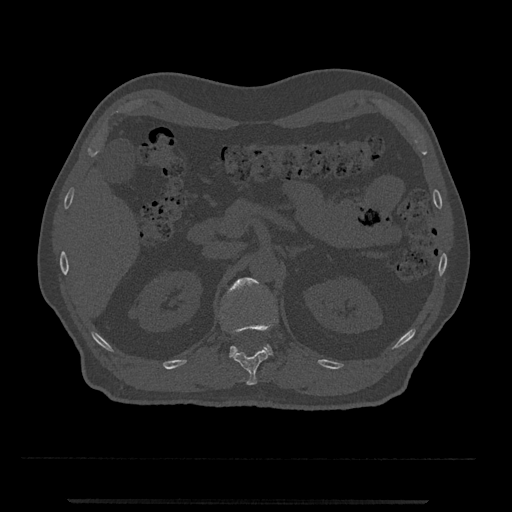
CT including the spine, one axial slice. Slice 374 of 797 in the series (ordered by position). Reconstruction kernel Br40s/3. Bone window (W 1800 / L 400 HU). 0.5 mm slice thickness. 512 × 512 image matrix. Male patient, age 63 years. Case-level facts recorded for this patient, not image findings: primary cancer: prostate.
Outlined on this slice (semi-automatic segmentation, software-assisted and operator-edited):
- L1 vertebra: bounding box [x1, y1, x2, y2] px = [227, 277, 275, 358]
- T12 vertebra: [232, 320, 278, 385]